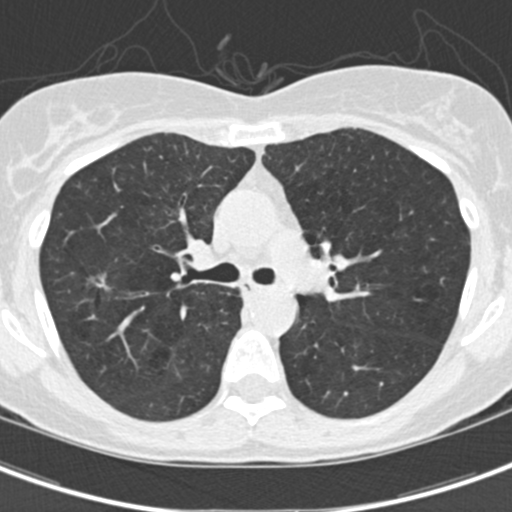
Low-dose screening chest CT, one axial slice. Position 100 of 154 along the scan axis. 120 kVp. Lung window (W 1500 / L -600 HU). 2 mm slice thickness. 512 × 512 image matrix, field of view 280 × 280 mm.
Annotated regions visible in this slice (manually delineated by an expert):
- lesion 1 (tumor, upper lobe of right lung): bounding box (x1, y1, x2, y2) in pixels: (87, 272, 110, 290)